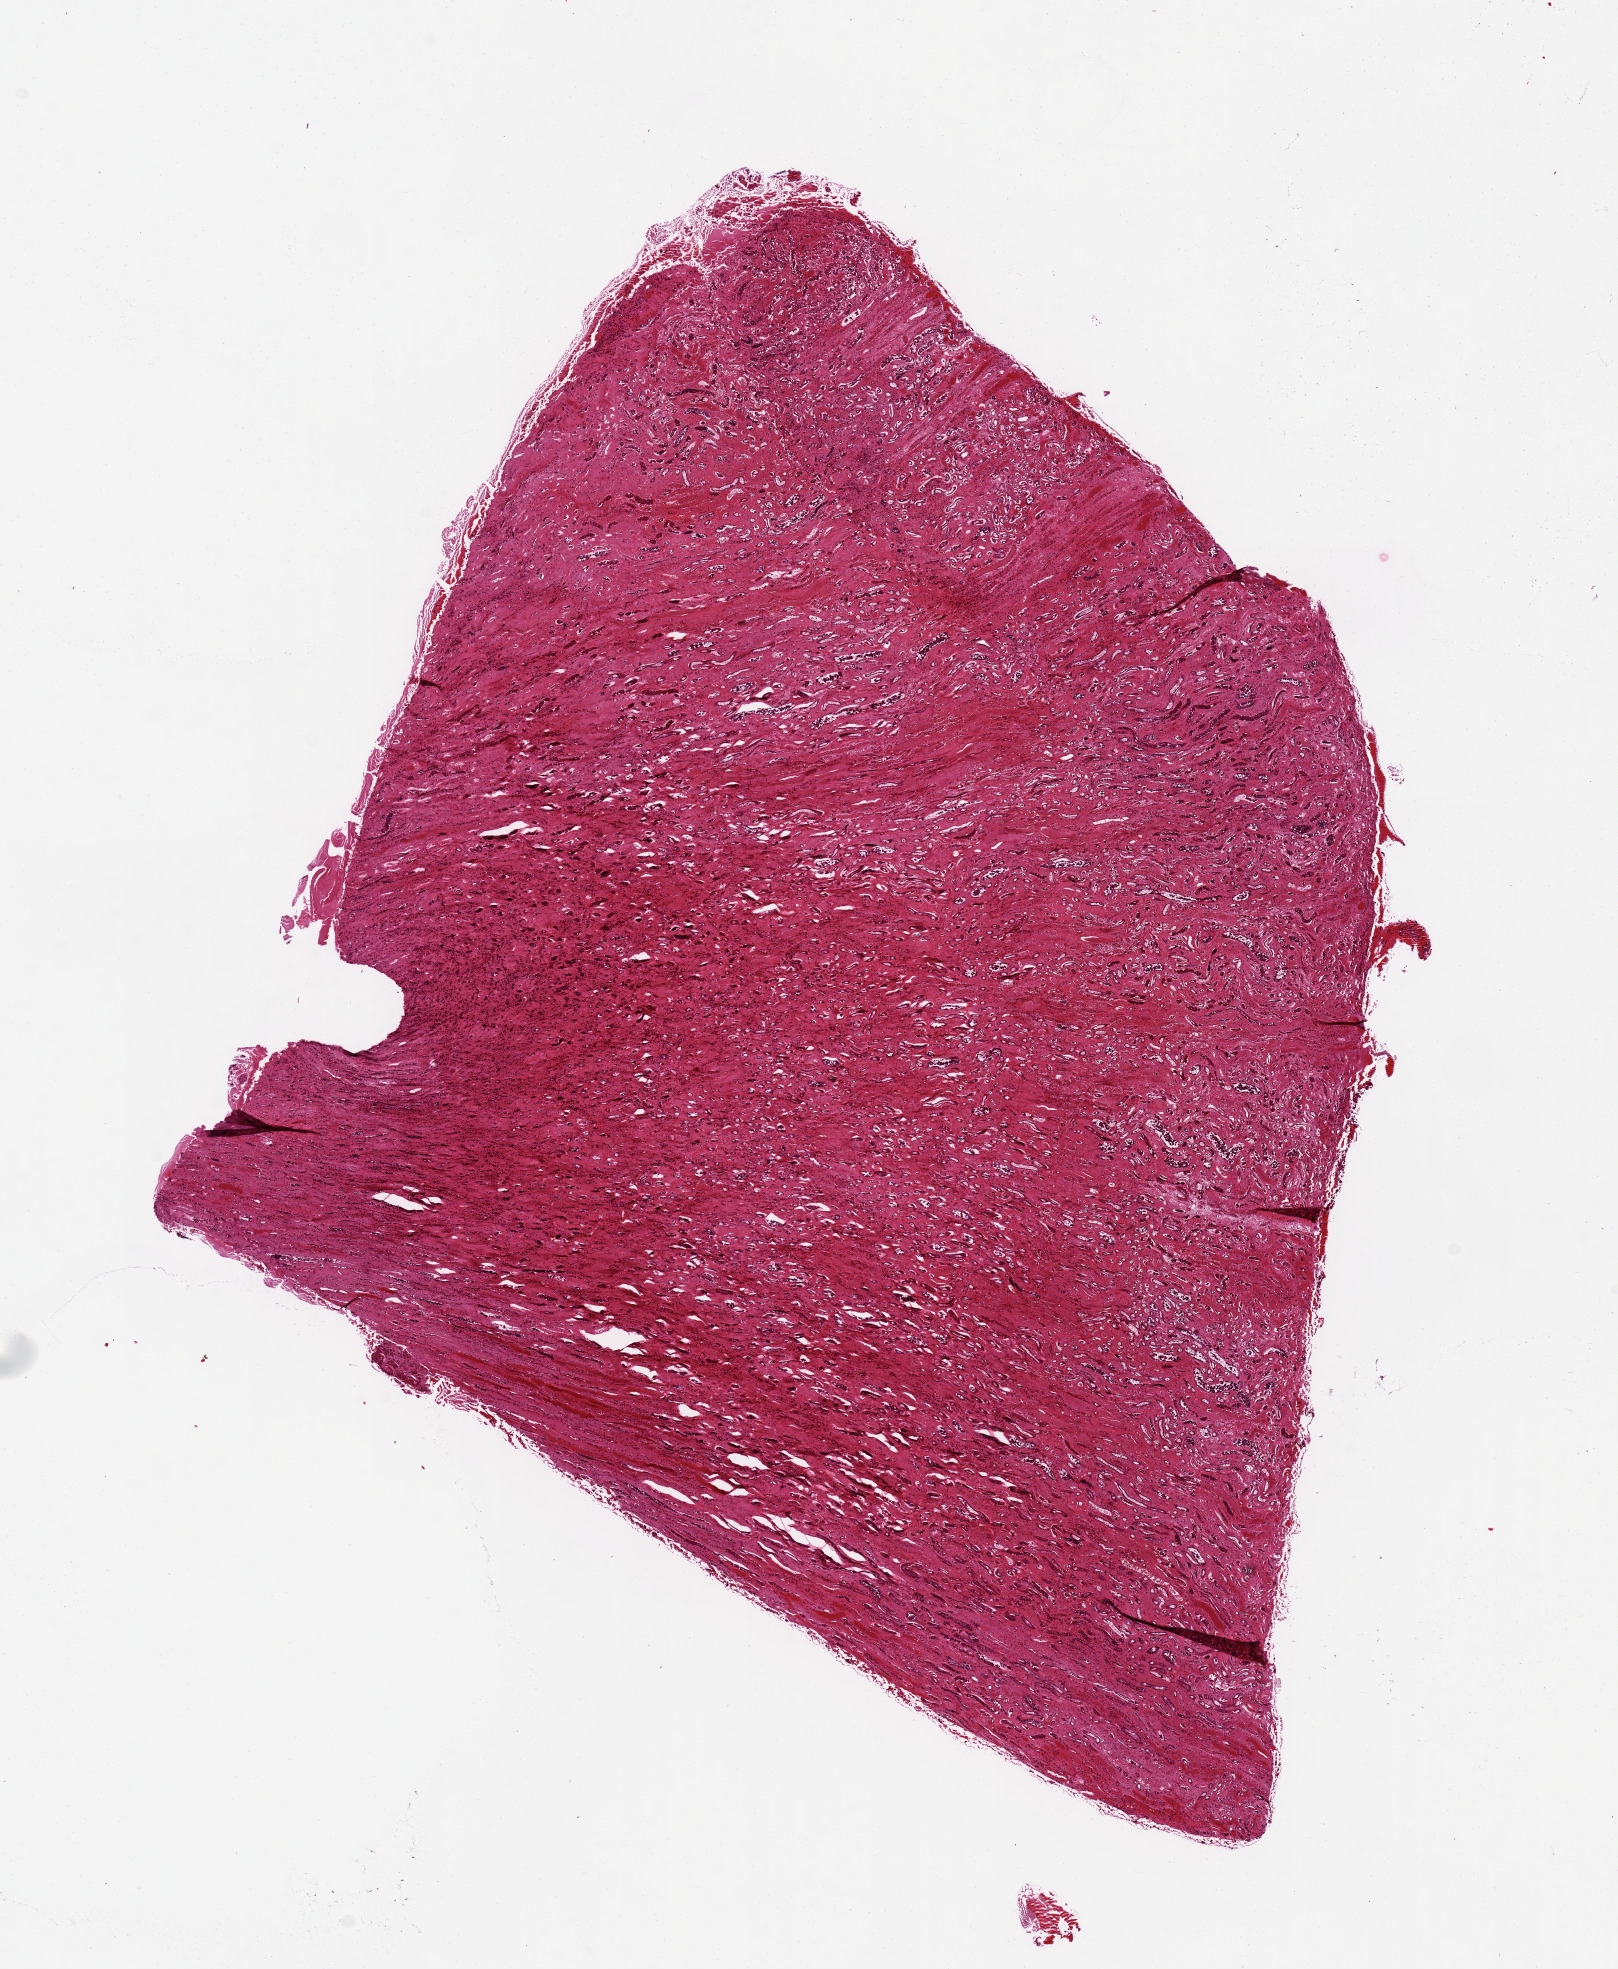
Digitized H&E-stained section, brightfield, shown as a low-resolution overview of the whole scanned area (about 12.8 x 15.6 mm, from a 20x scan); PAXgene-fixed paraffin-embedded (PFPE) section; section of renal medulla (target tissue); donor tissue sample. Female donor.
- pathologist's review note for this sample: Marked interstitial fibrosis